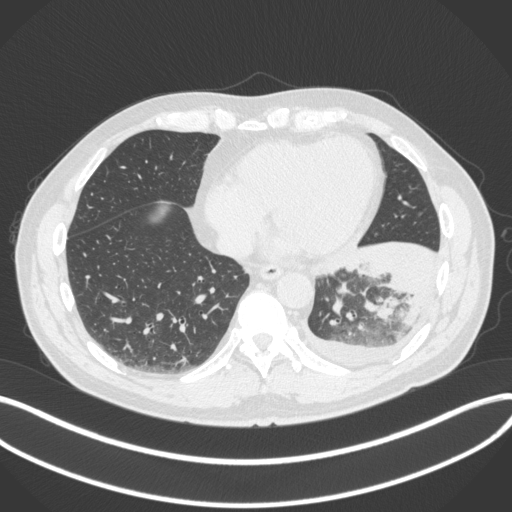
Chest CT, one axial slice. Slice 106 of 350 in the series (ordered by position). Lung window (W 1500 / L -600 HU). 1 mm slice thickness. 512 × 512 image matrix, field of view 400 × 400 mm. Patient: male, 58 years. From the clinical record (not read from this slice): clinical TNM (as recorded): T3 N1 M1b; histopathological grade: G3.
Structures marked on this image (rectangle marked by the reading radiologist):
- lung tumour (recorded histology: small cell carcinoma): box from (x=332, y=279) to (x=350, y=319) px